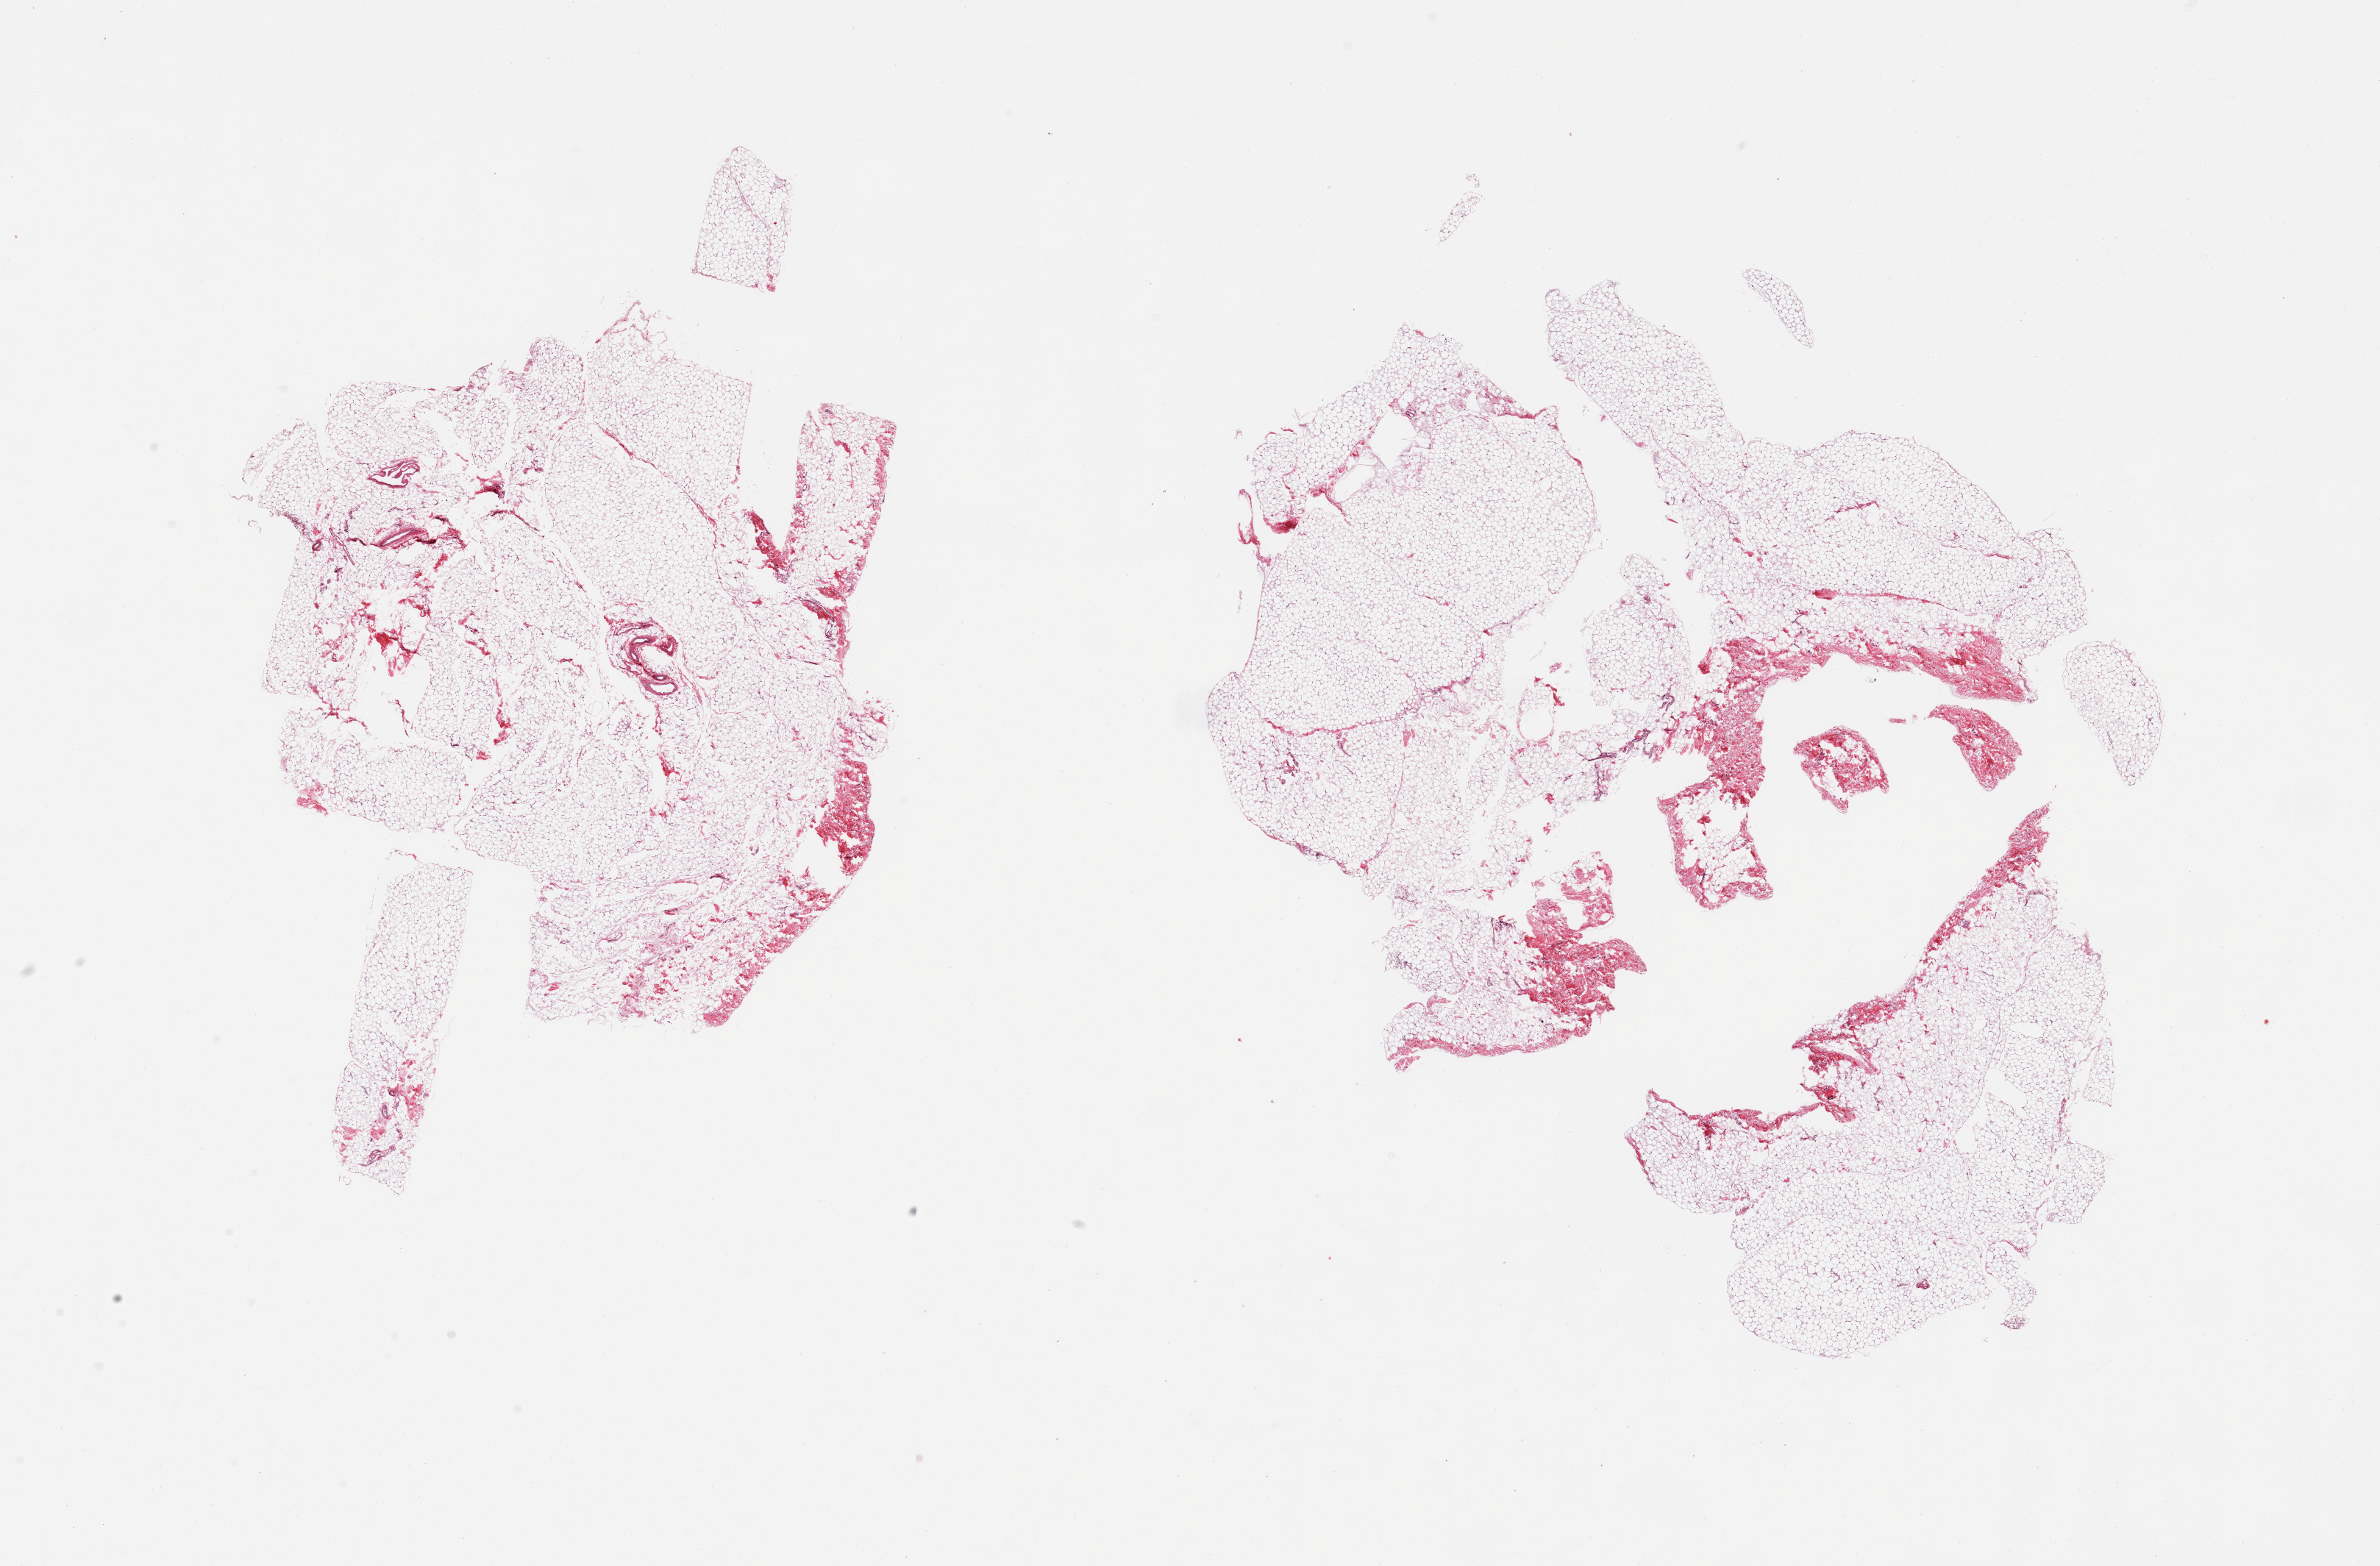
Digitized haematoxylin and eosin-stained section — shown as a low-resolution overview of the whole scanned area (about 25.6 x 16.8 mm, from a 20x scan), PAXgene-fixed, paraffin-embedded tissue, section of omentum (target tissue), donor tissue sample. Male donor.
• pathologist's review note for this sample: 2 pieces; mature adipose tissue with small portion of fibrous tissue/small vessels